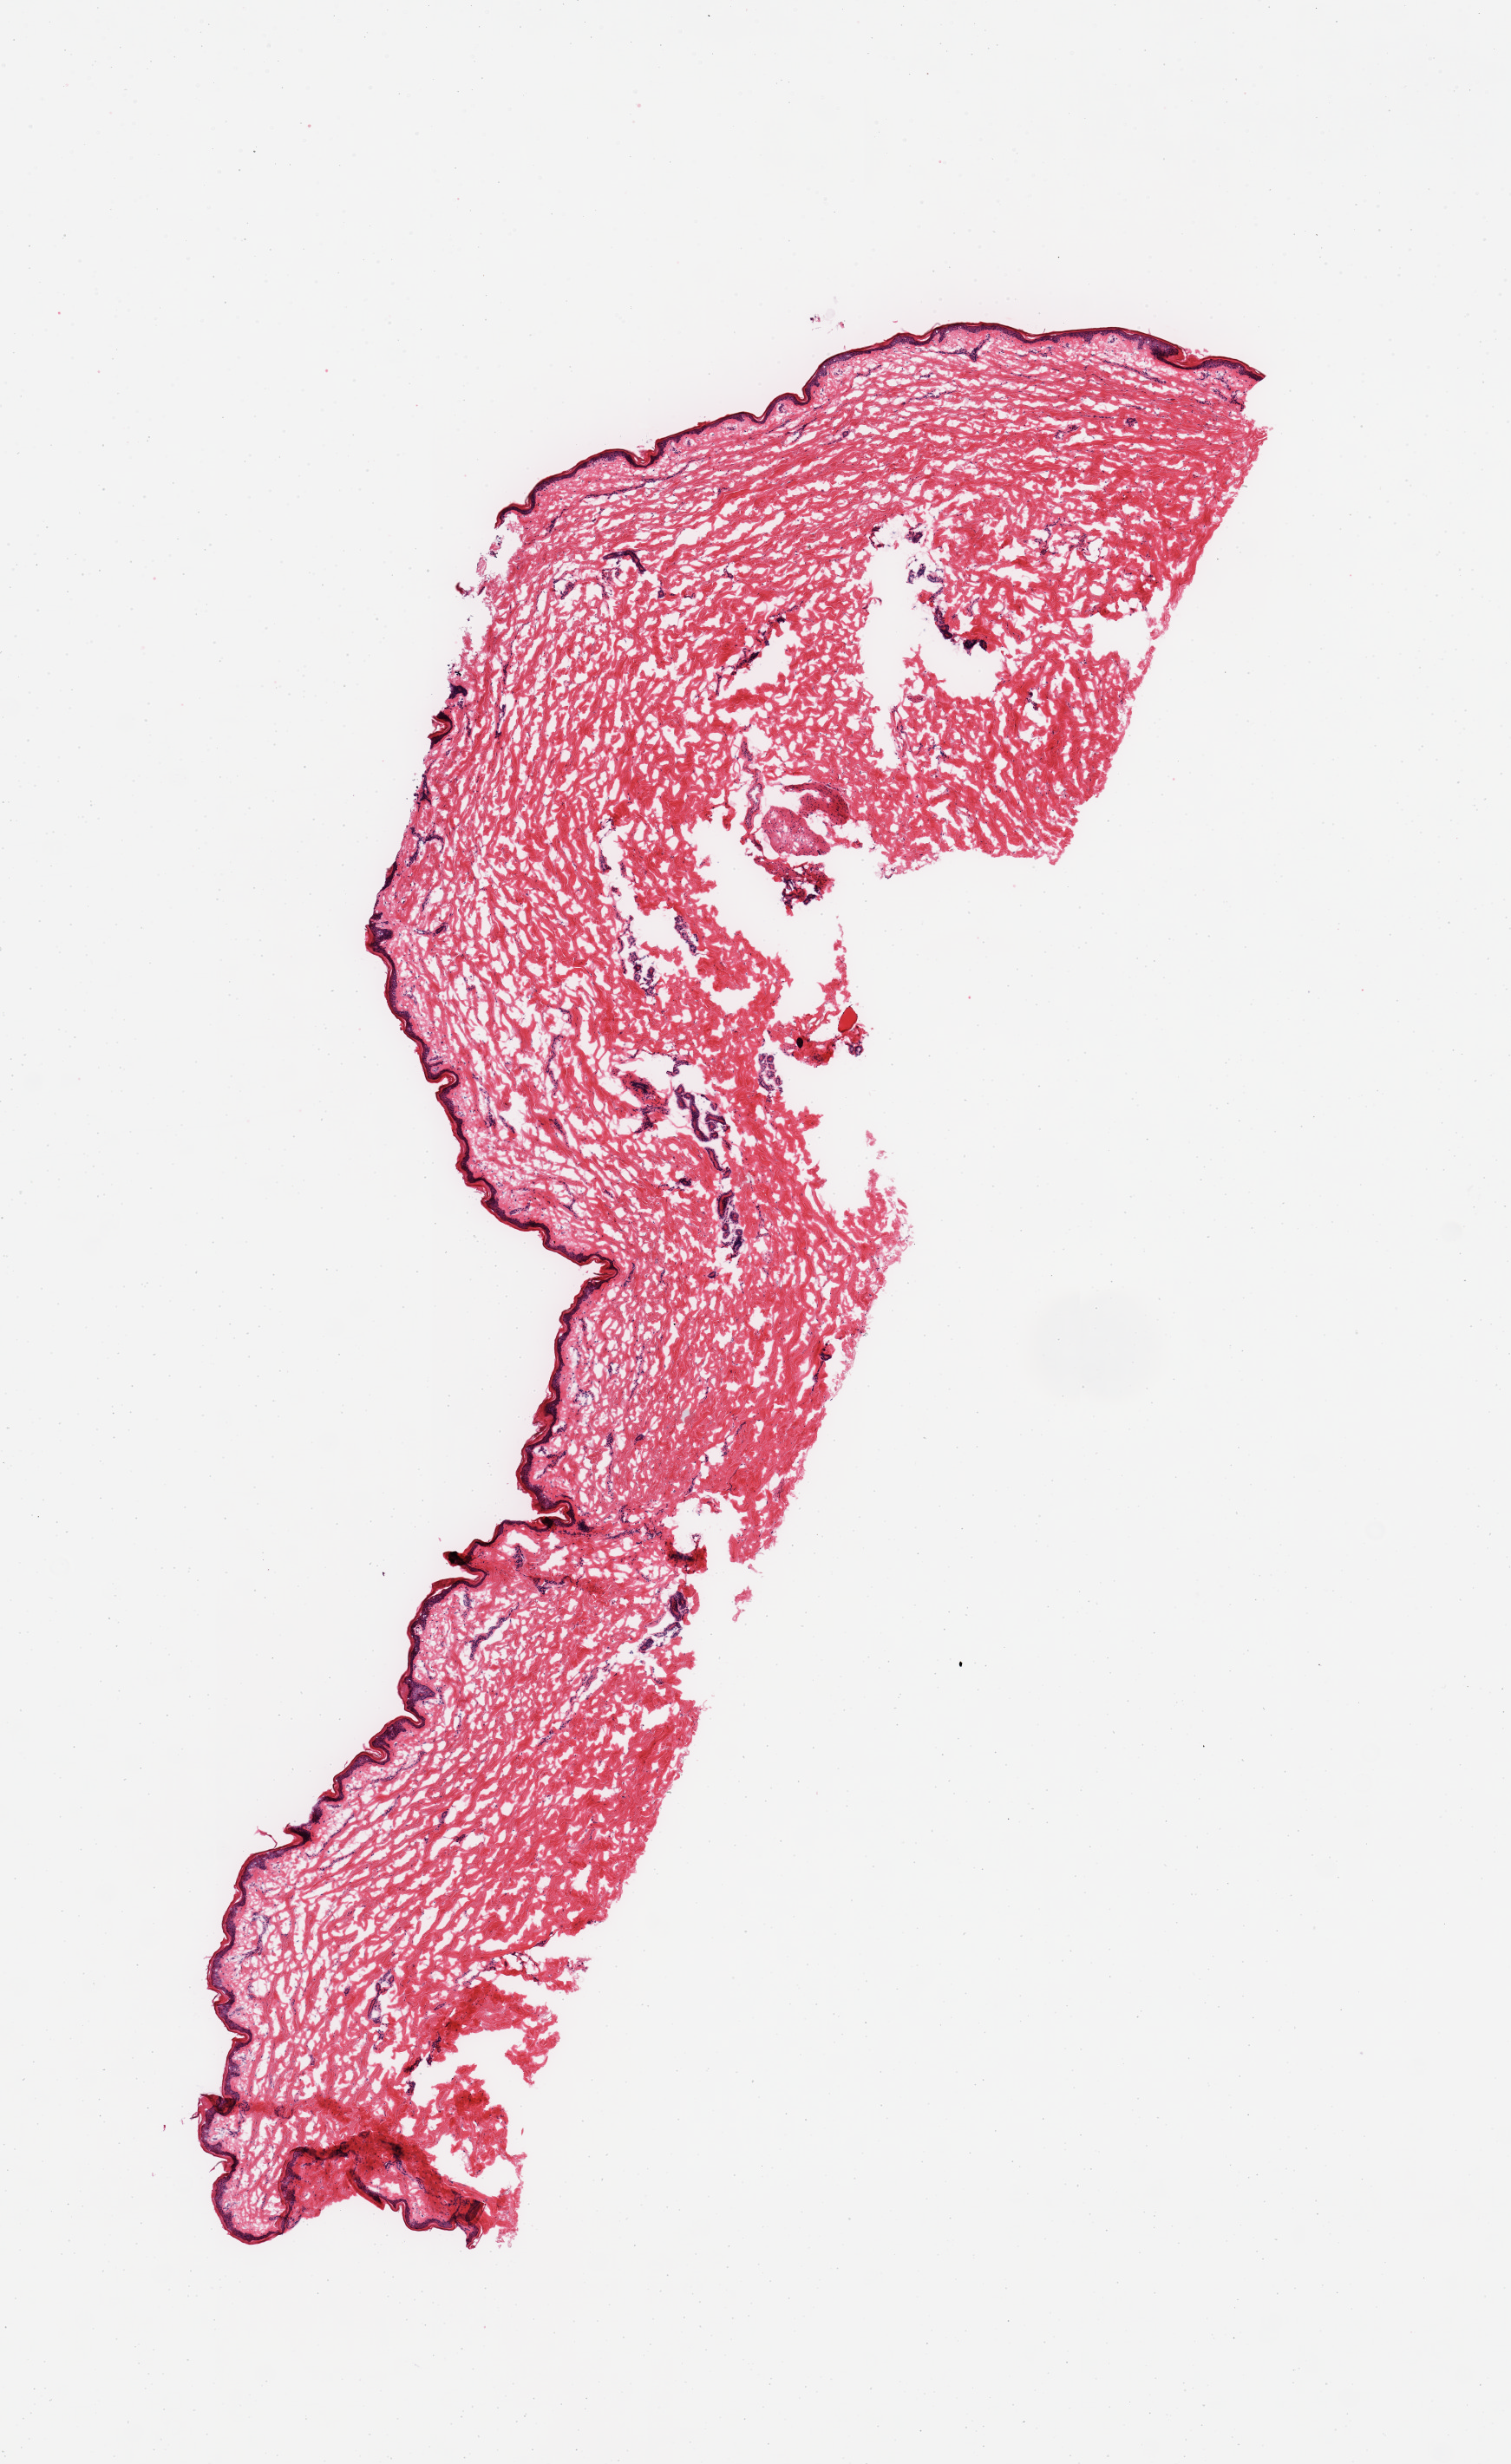
Haematoxylin and eosin whole-slide image — whole scanned area (about 6.9 x 11.2 mm) shown as a low-resolution overview. Frozen section. Sampled site (target tissue): skin of lower leg. Tissue donor sample. Donor sex: female.
- pathologist's review note for this sample: 1 piece; comparable to content in PAXgene sample